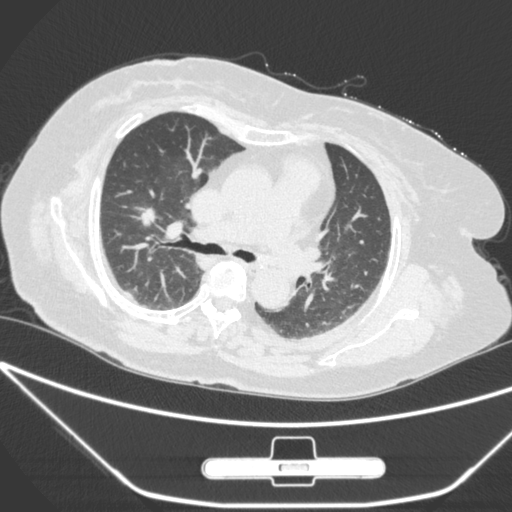
Chest CT, one axial slice; position 165 of 245 along the scan axis; 120 kVp; lung window (W 1500 / L -600 HU); 1 mm slice thickness; 512 × 512 image matrix, field of view 365 × 365 mm. Patient: female, 65 years. Case-level facts recorded for this patient, not image findings: clinical TNM (as recorded): T1c N0 M0; histopathological grade: G3.
Outlined on this slice (rectangle marked by the reading radiologist):
- lung tumour (recorded histology: adenocarcinoma): bounding box (x1, y1, x2, y2) in pixels: (132, 198, 165, 244)